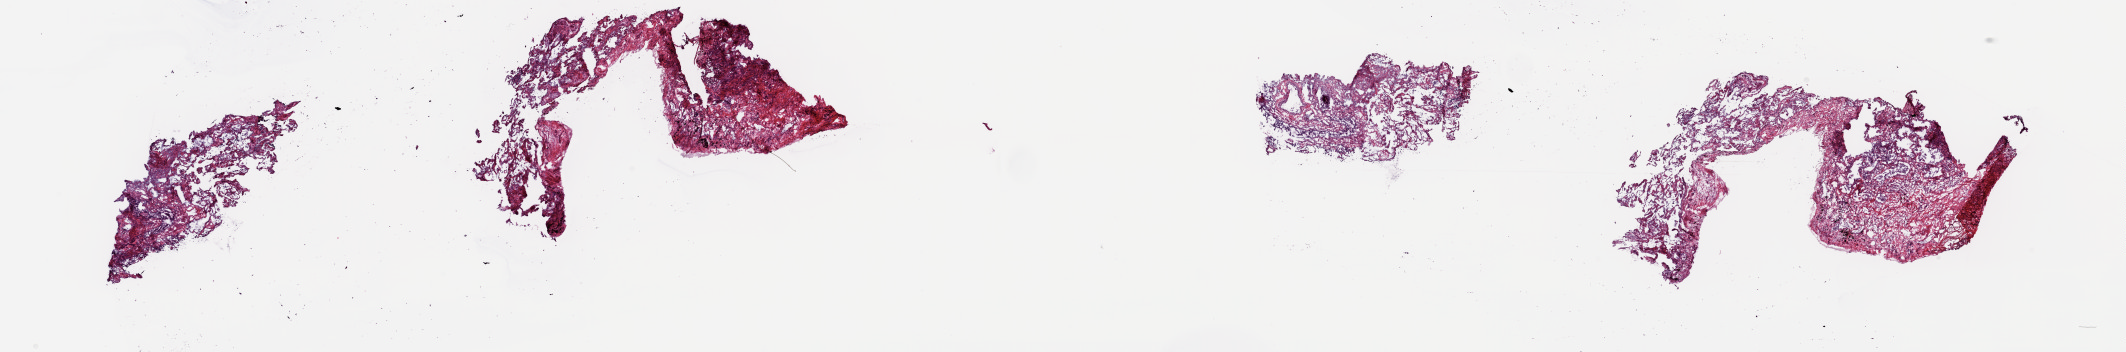
Whole-slide histology image, H&E — shown as a low-resolution overview of the whole scanned area (about 33.7 x 5.6 mm); frozen section from the top of the tissue portion; solid tissue normal (non-tumour tissue) sample from the lung. Patient: female, age at initial diagnosis 65 years. Composition of this section per pathologist review: tumour cells 0%, tumour nuclei 0%, normal cells 35%, stromal cells 65%, necrosis 0%. Infiltration values recorded for this section: lymphocyte infiltration 8%, monocyte infiltration 5%, neutrophil infiltration 3%.
This section: solid tissue normal (non-tumour) sample from the same patient. Patient diagnosis: Squamous cell carcinoma, NOS (upper lobe, lung).